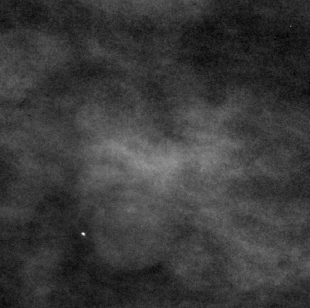
Region of interest cut from a scanned film mammogram (one marked finding), right breast, CC view.
Mass, shape lobulated, margins circumscribed; BI-RADS assessment category 3; benign; no additional work-up was recommended (benign without callback).